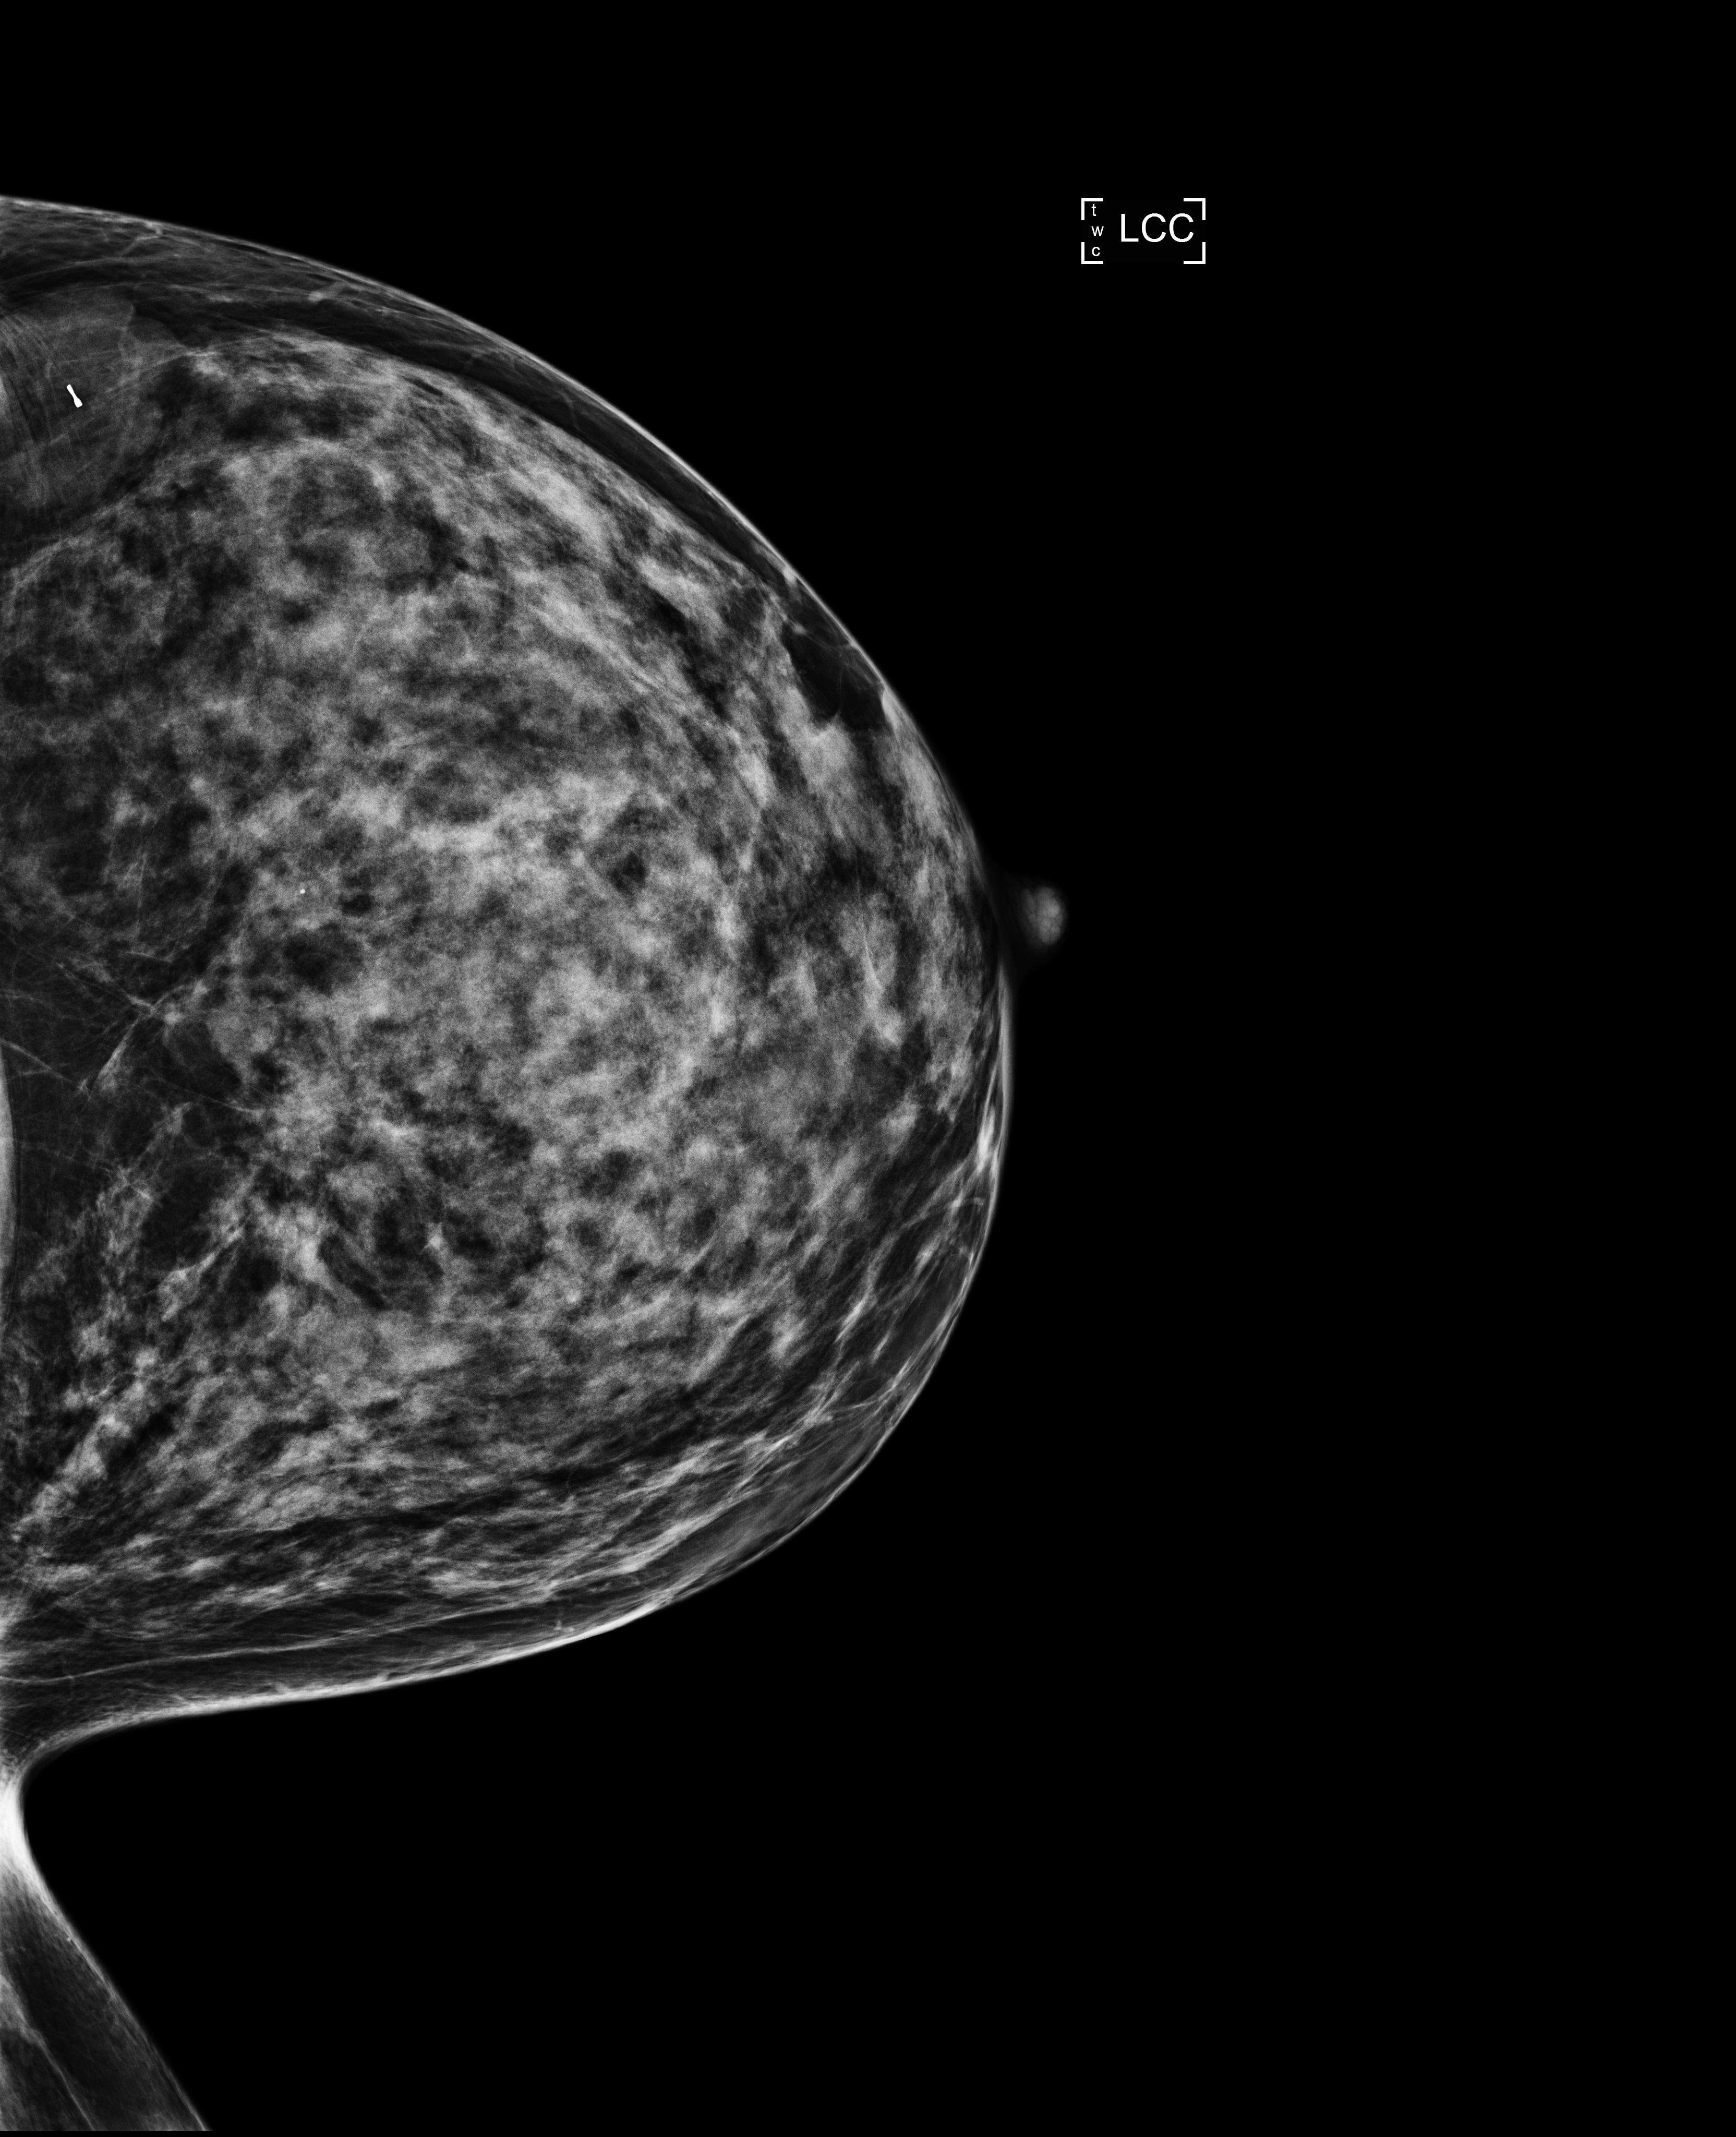
Full-field digital mammogram (FFDM); left breast; cranio-caudal projection; screening examination. Patient: female, 44 years.
Breast density at the screening exam (both breasts): heterogeneously dense (BI-RADS density category c). Final BI-RADS assessment for this screening round (tomosynthesis exam, both breasts): category 2. Recall: no recall after this screen.